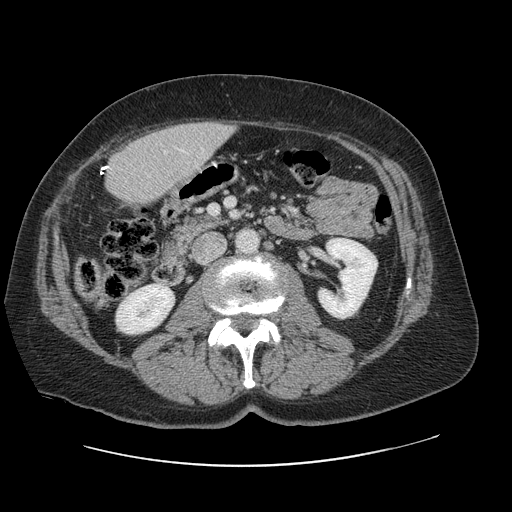
Contrast-enhanced abdominal CT, one axial slice. Slice 24 of 138 in the series (ordered by position). Intravenous contrast given. Soft-tissue window (W 400 / L 40 HU). 512 × 512 image matrix, field of view 402 × 402 mm. Male patient, age 71 years. From the clinical record (not read from this slice): diagnosis: colorectal cancer liver metastases, imaged before liver resection; multiple liver metastases: no; largest metastasis: 3.3 cm; chemotherapy before resection: no.
Outlined on this slice (expert manual segmentation):
- liver: bounding box [x1, y1, x2, y2] px = [106, 122, 232, 208]
- planned liver remnant (the part of the liver to remain after resection): [105, 134, 178, 207]